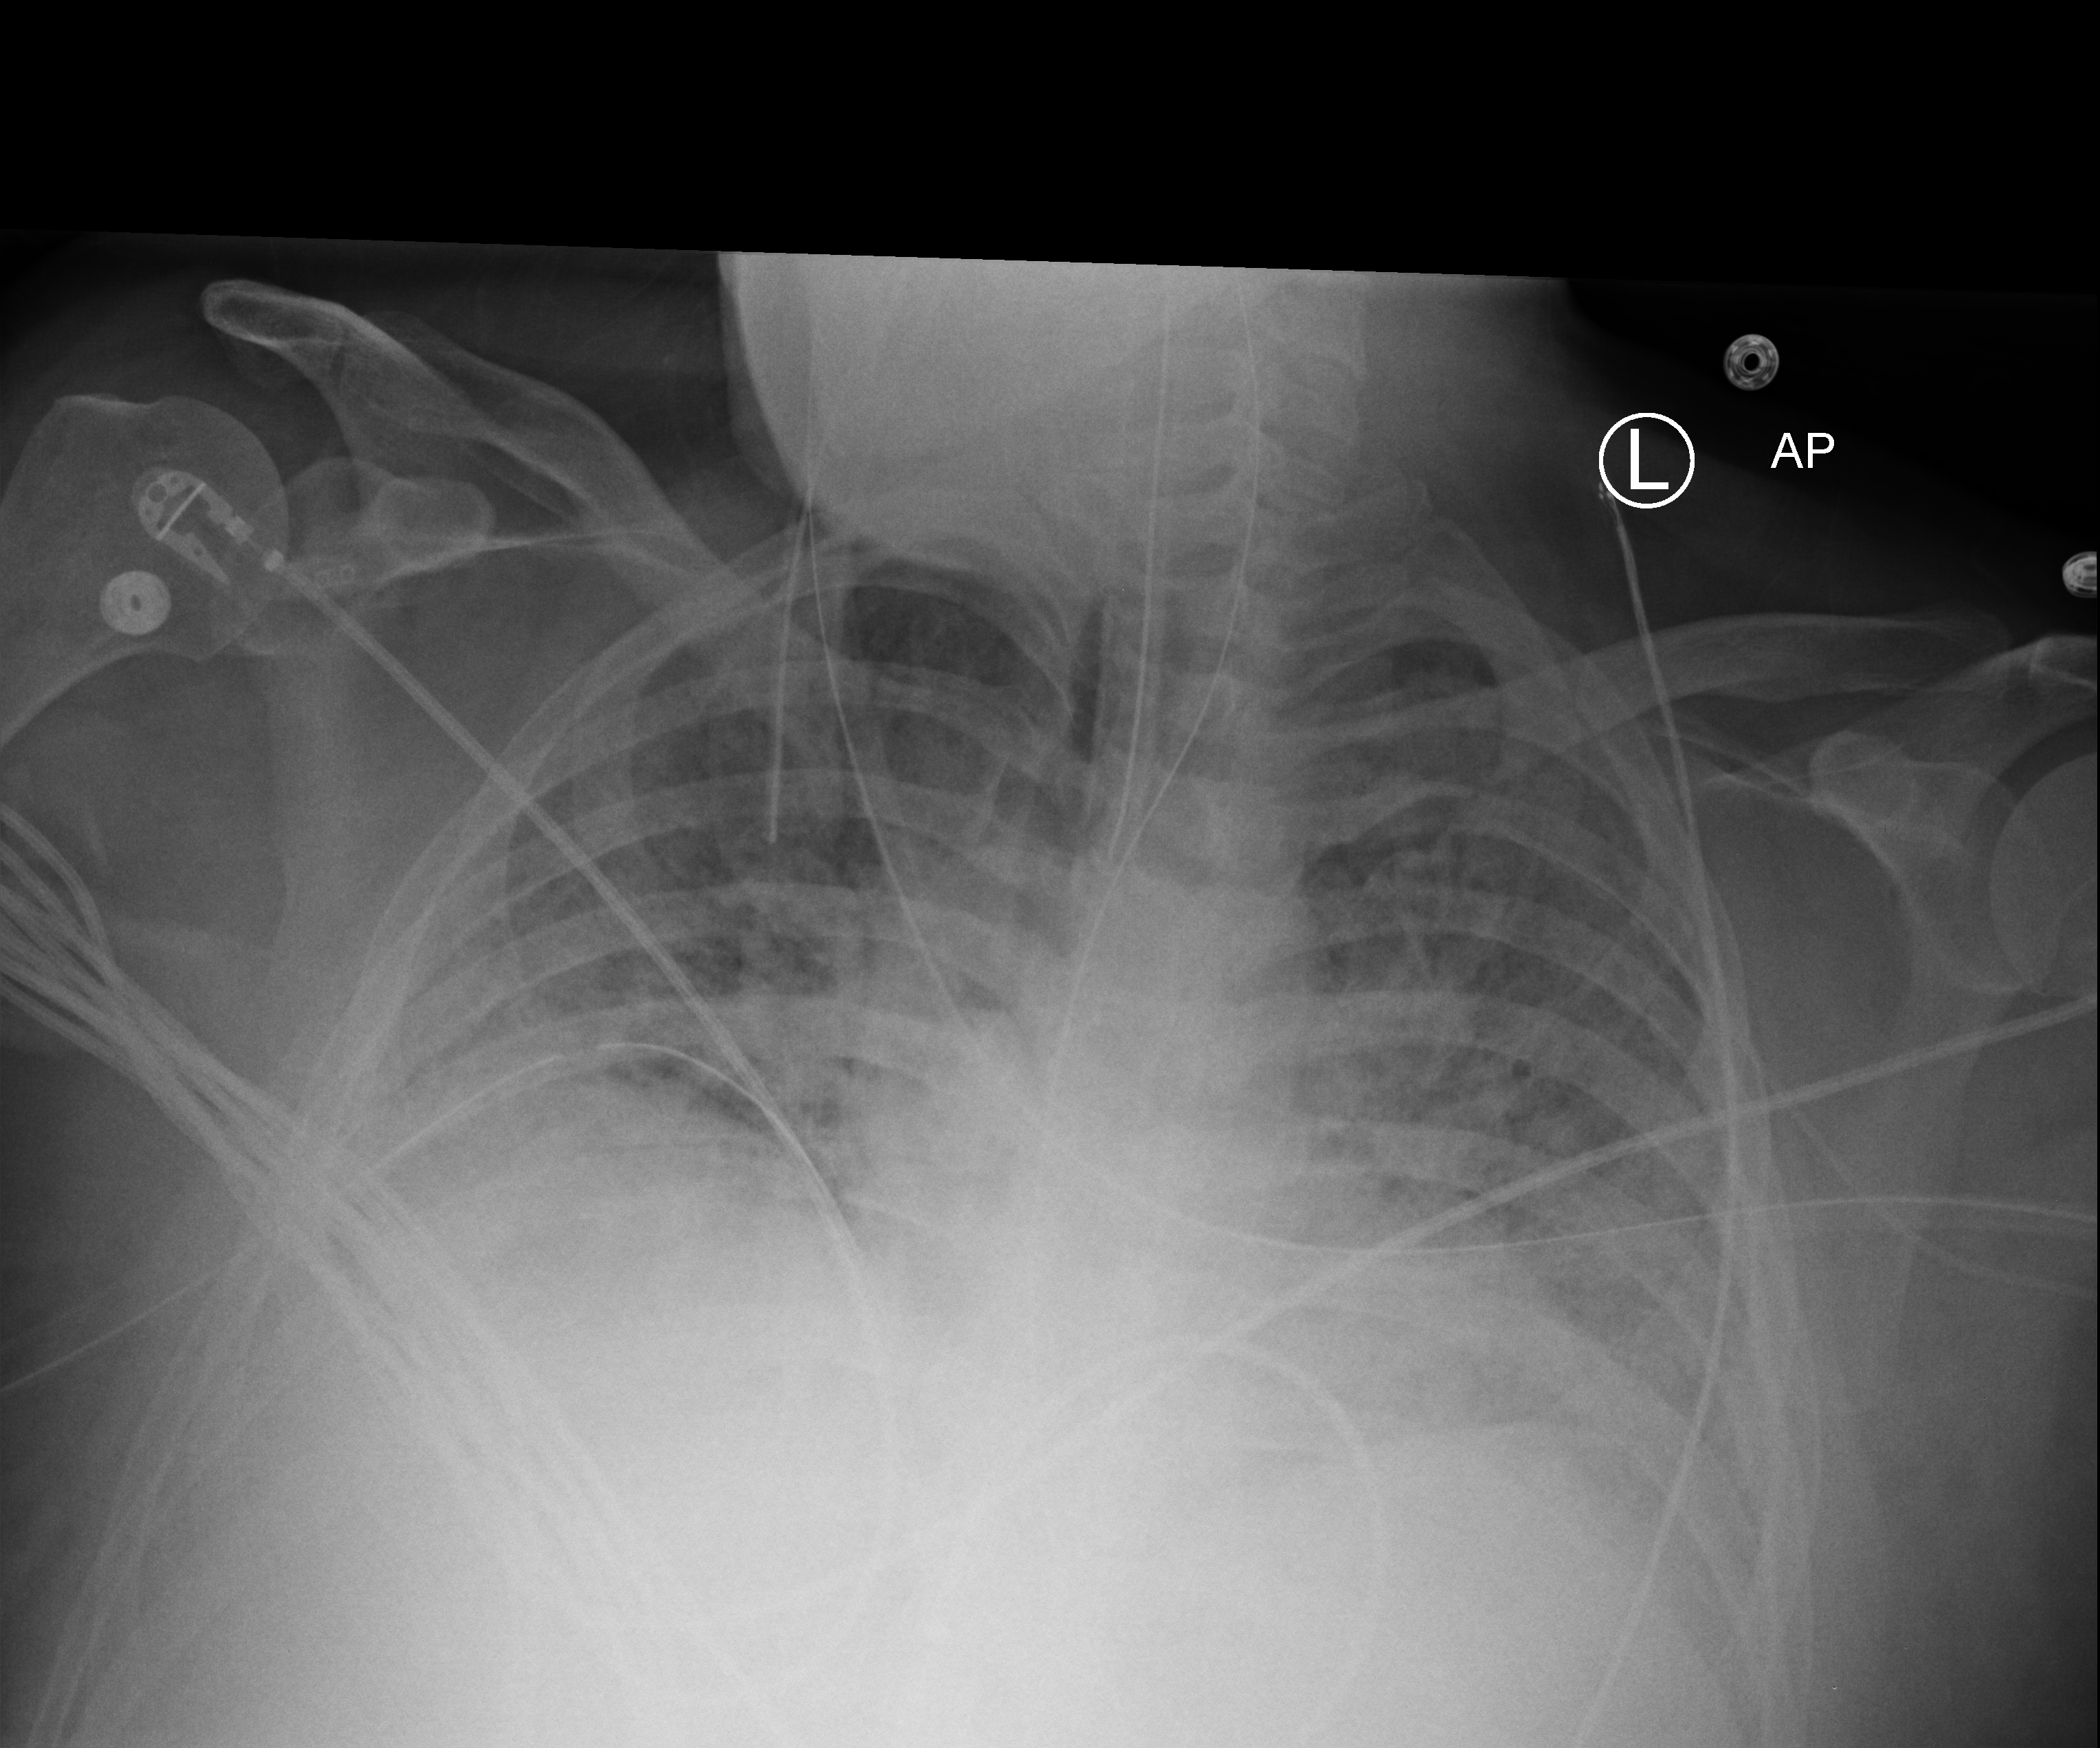
Chest X-ray (portable), anteroposterior (AP) projection. Male patient hospitalised with COVID-19, age 18–59 years.
Admission-level facts for this patient (not findings on this image; timing relative to this image not recorded):
- mechanically ventilated during this hospital stay: yes
- smoking status (admission record): never
- admitted to intensive care during this hospital stay: yes